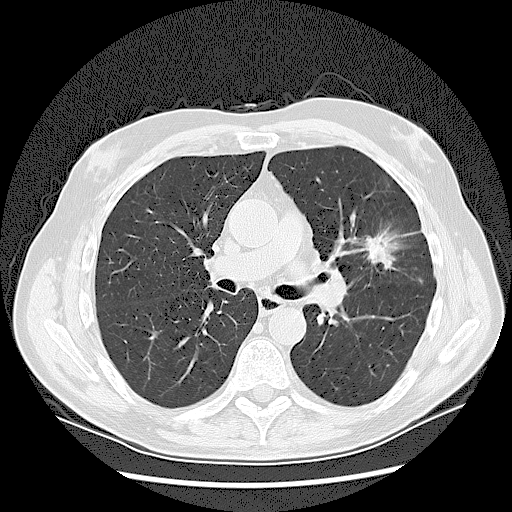
Chest CT (low-dose screening protocol), one axial image. Baseline screening round. Lung window (W 1500 / L -600 HU). 2.5 mm slice thickness. Slice 56 of 132 in the series. 512 × 512 image matrix, field of view 380 × 380 mm. Male, age 65 years at enrolment. Current smoker at enrolment.
- Expert reader's lesion annotation, bounding box (x1, y1, x2, y2) in pixels: (351, 228, 397, 272).
- The exam's reader record, not a measurement of the box and not confirmed to be the same lesion: non-calcified nodule or mass ≥4 mm, left upper lobe, 37 × 27 mm, spiculated (stellate) margins, soft tissue attenuation.
- Lung cancer was diagnosed 56 days after this screen: non-small cell carcinoma, poorly differentiated (G3), stage IA (AJCC 6th edition).